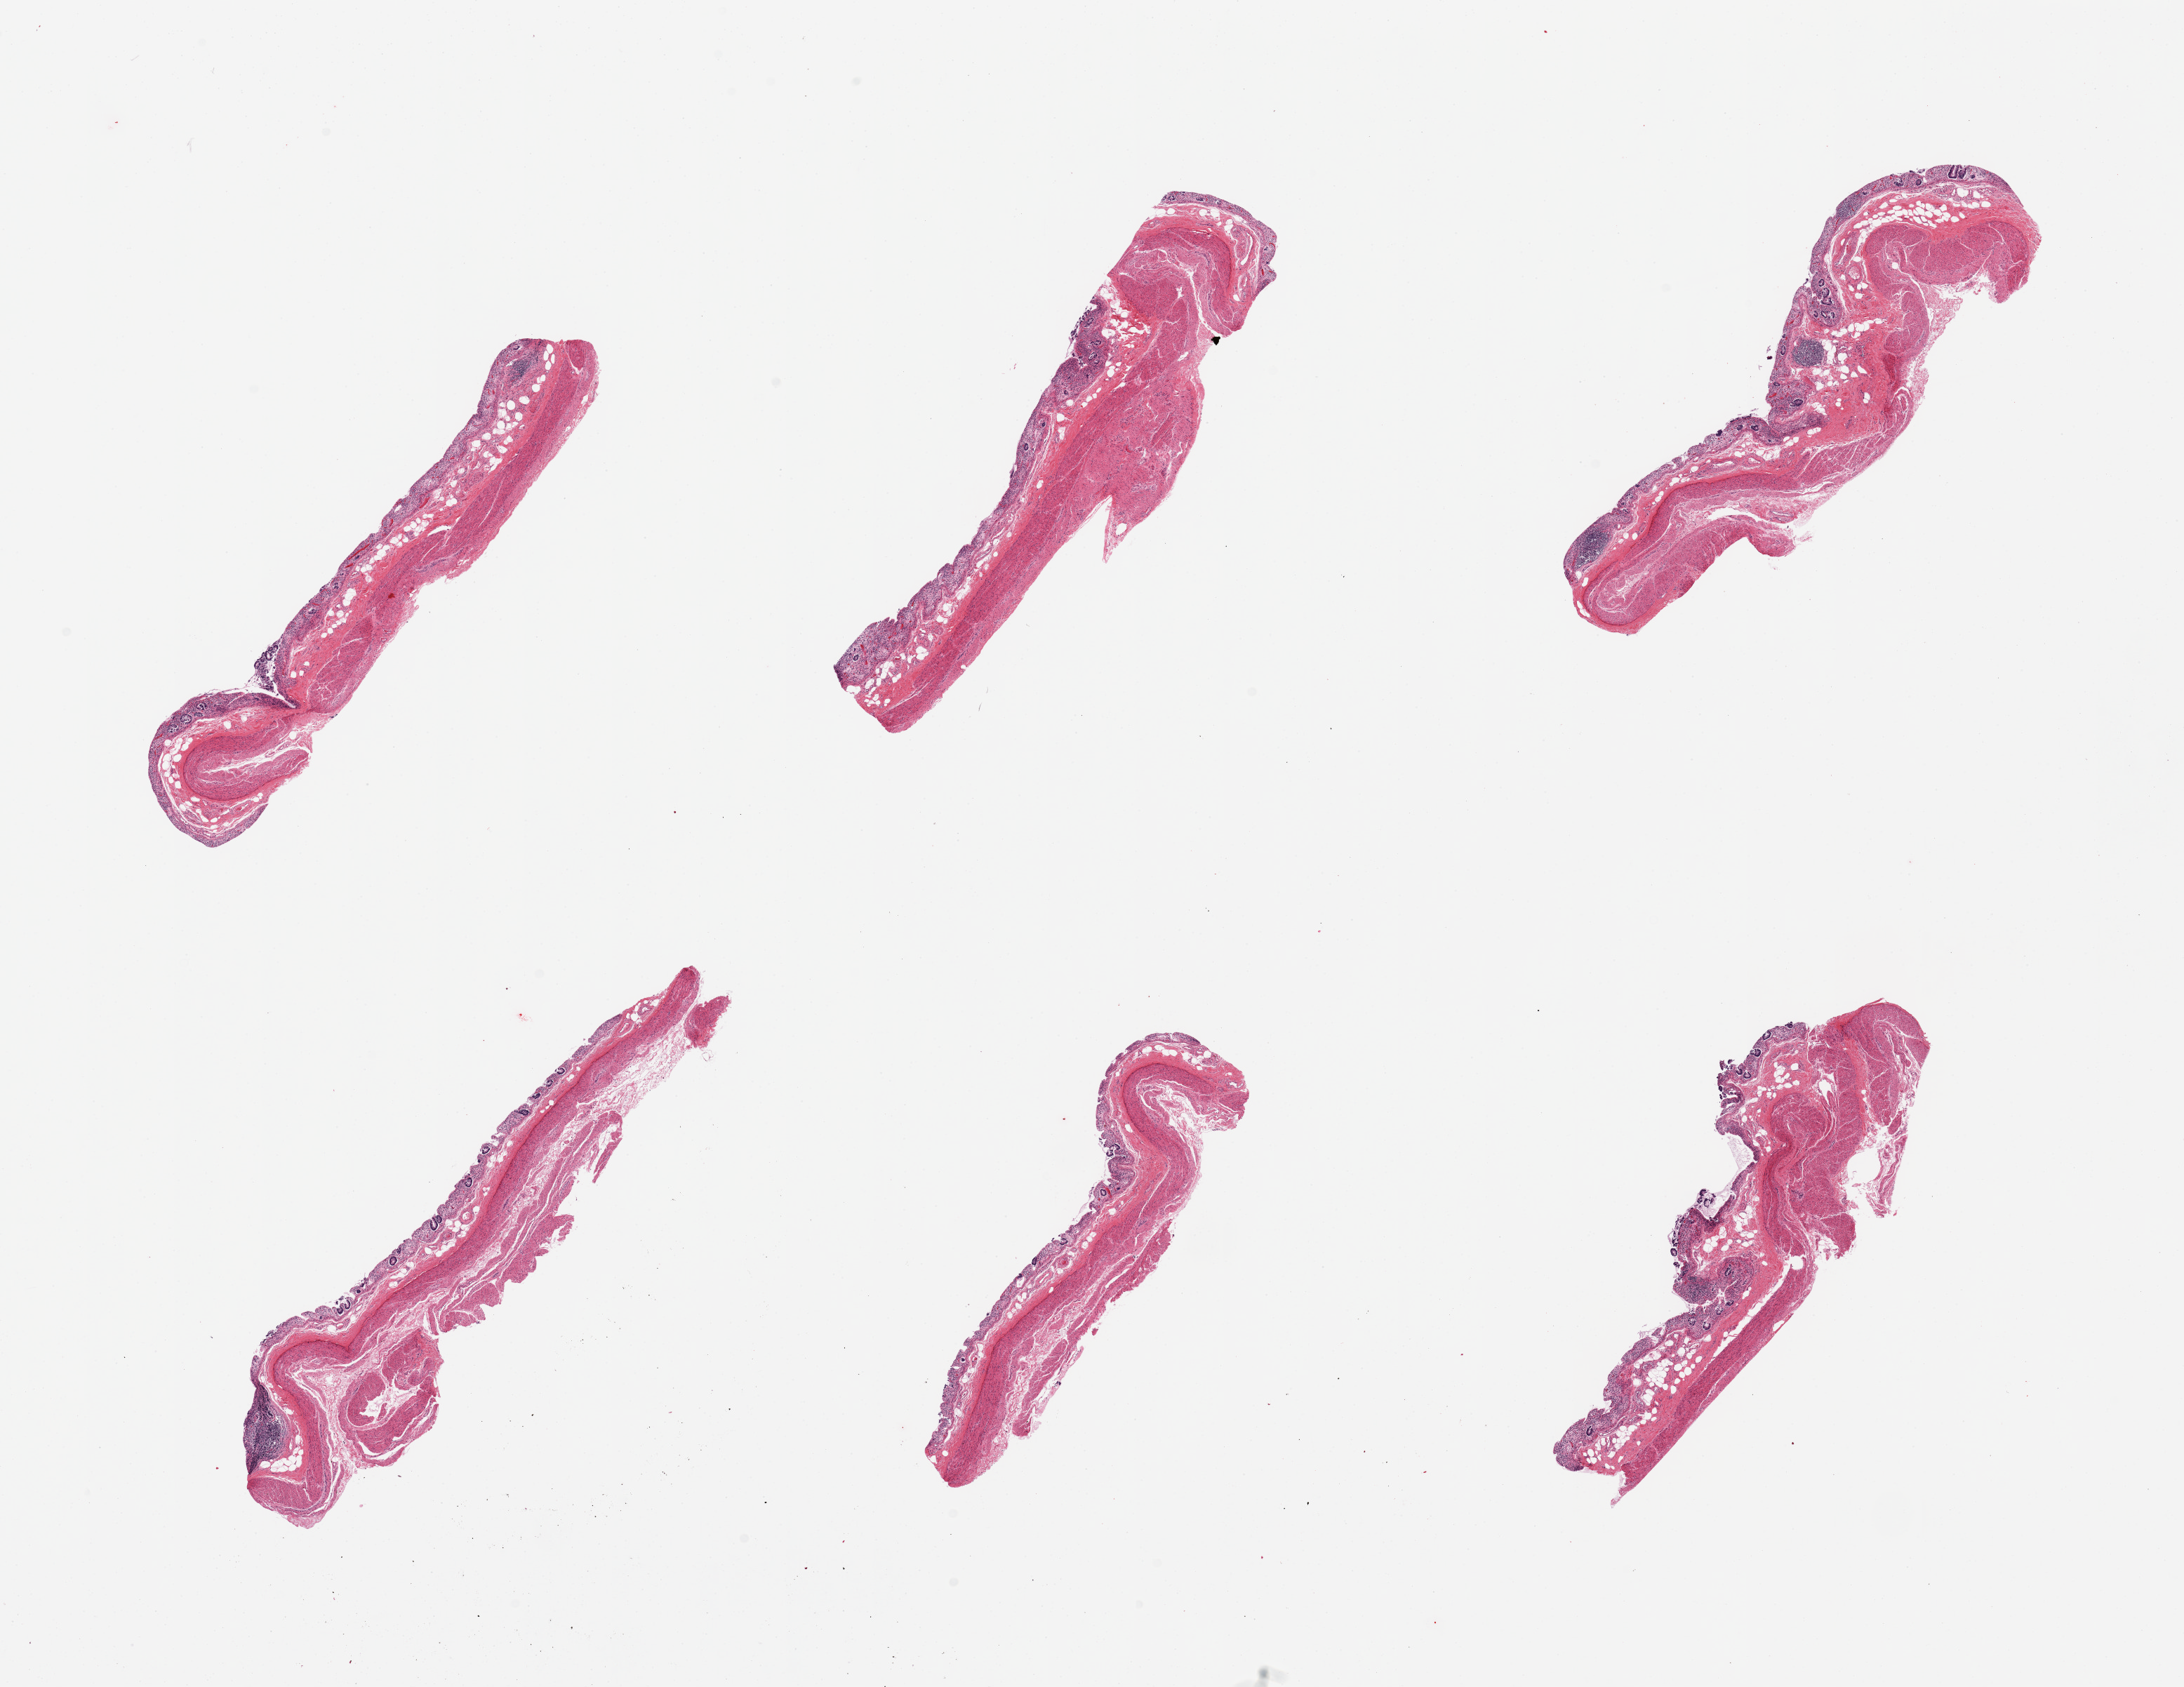
Digitized hematoxylin and eosin (H&E)-stained section, brightfield — whole scanned area (about 24.6 x 19.0 mm) shown as a low-resolution overview; PAXgene-fixed paraffin-embedded (PFPE) section; section of transverse colon (target tissue); tissue donor sample.
Review note (as recorded): 6 pieces; mucosa=3; muscle=1.